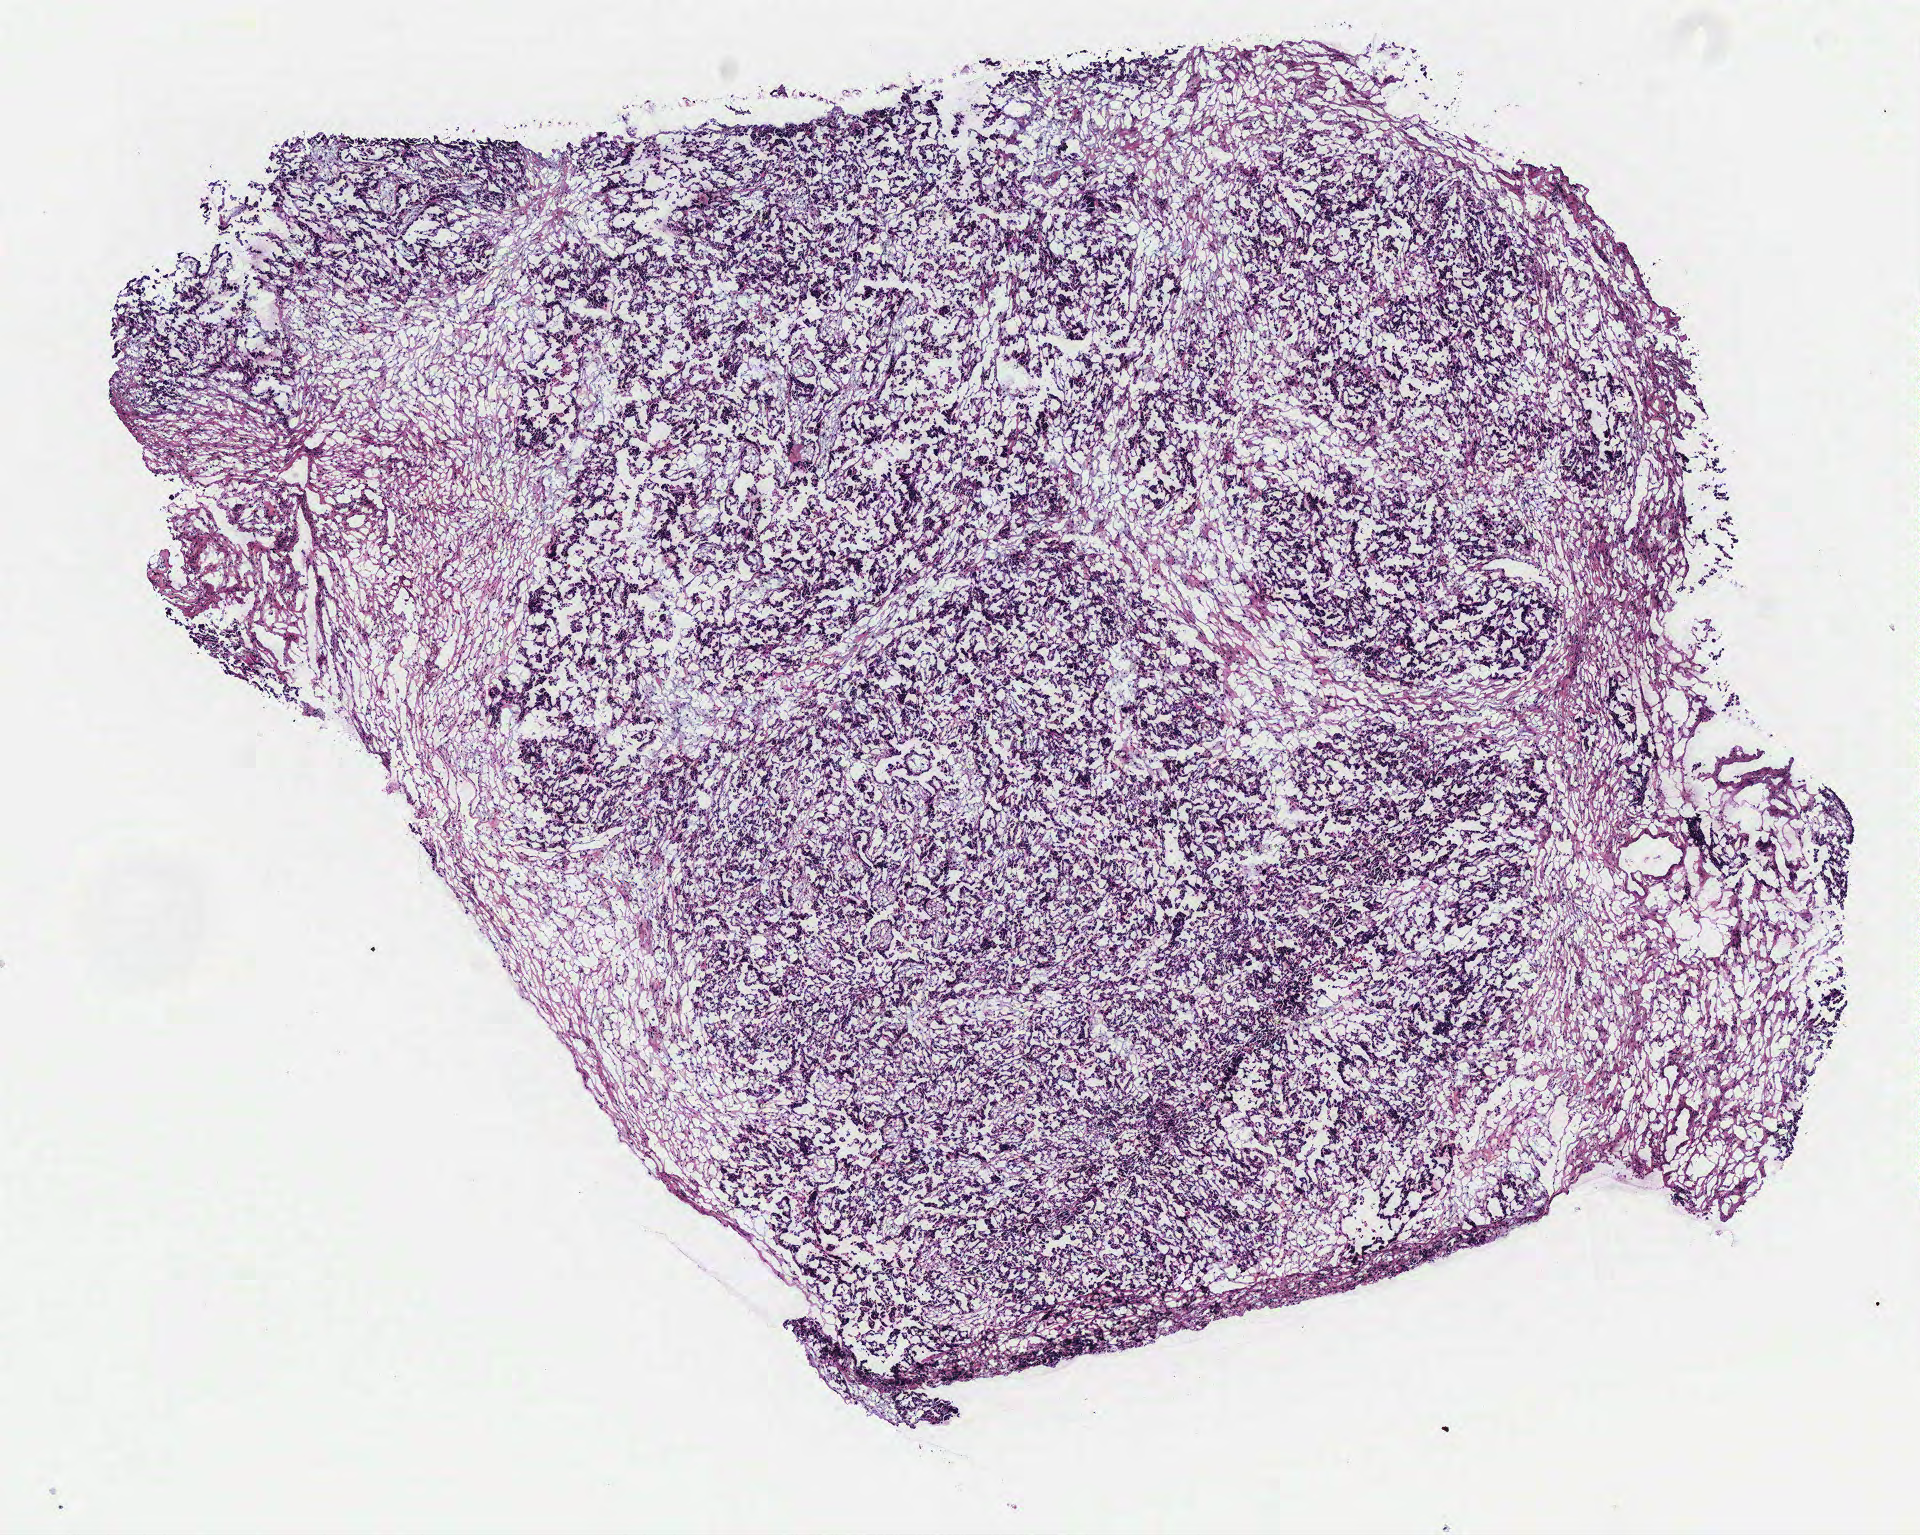
Digitized H&E tissue section (whole slide) — low-resolution overview of the scanned area, about 7.7 x 6.1 mm. Tumour tissue sample, ovary. Female, 74 y/o.
Histologic diagnosis: Serous adenocarcinoma, NOS. Primary tumour site (as recorded): peritoneum.